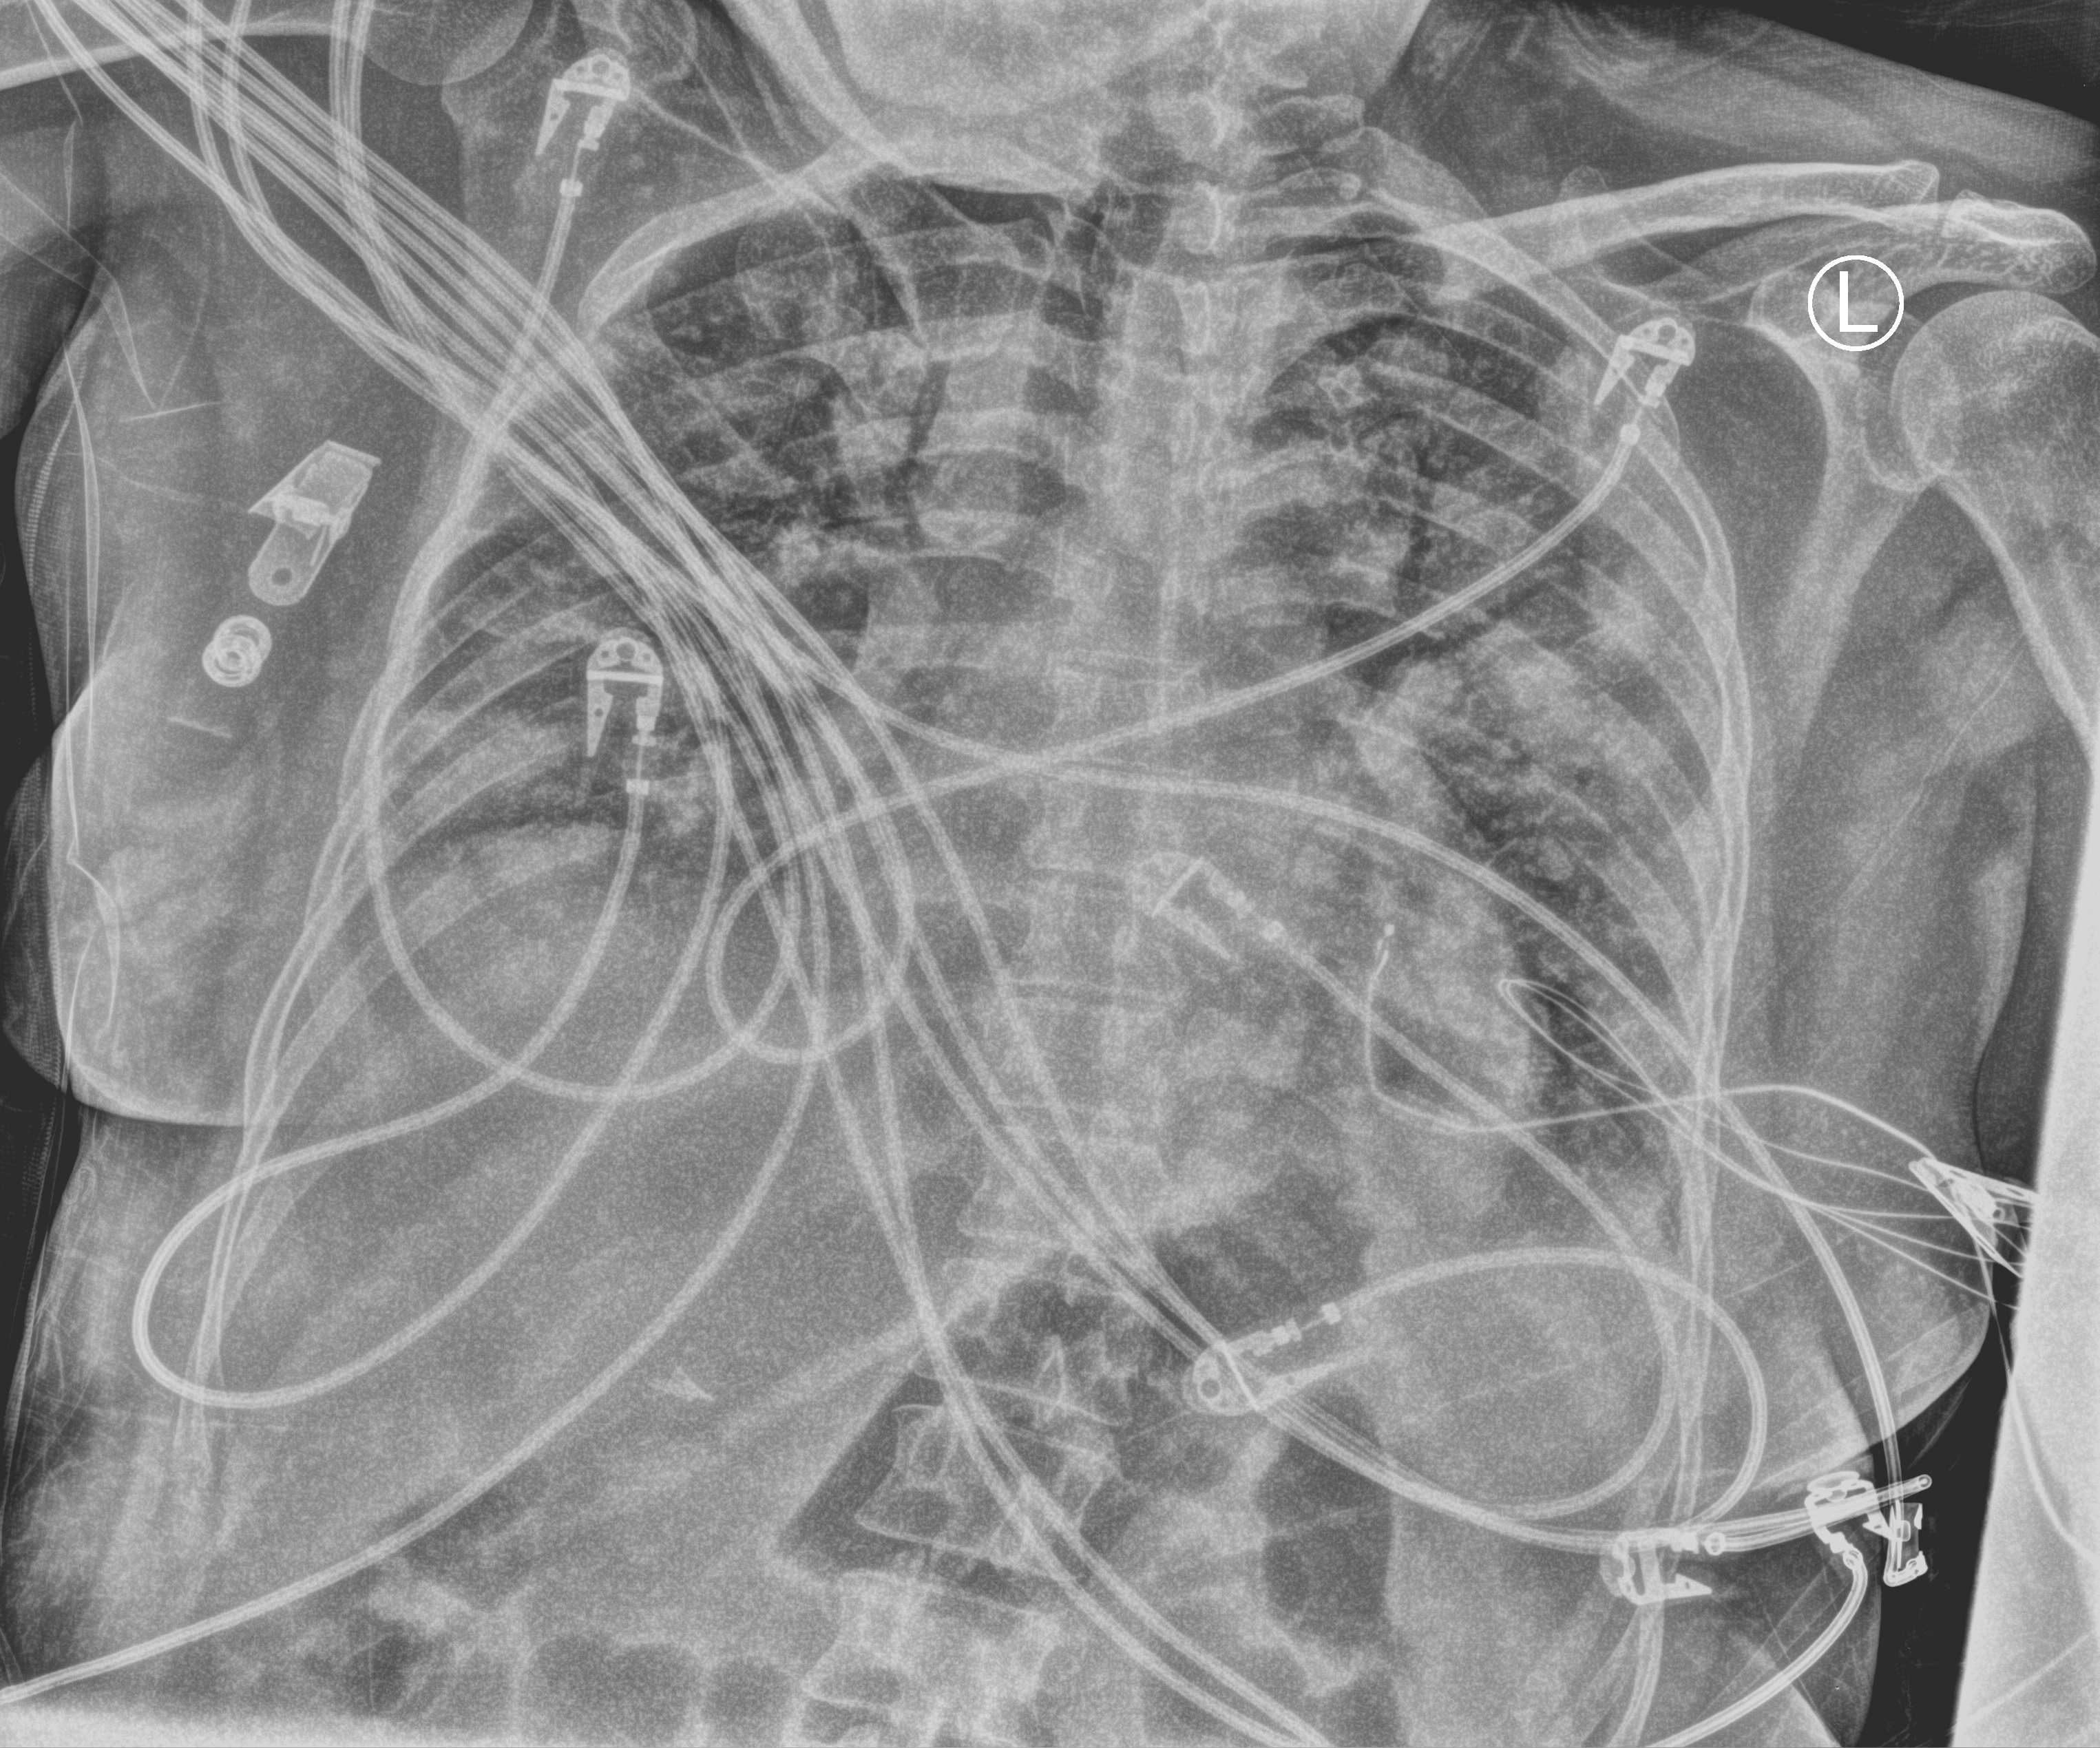
Bedside chest radiograph (computed radiography); anteroposterior (AP) projection. Patient hospitalised with COVID-19; female, aged 18–59 years.
Hospital-stay facts (about this admission, not read from this image; timing relative to this image not recorded): mechanically ventilated during this hospital stay: yes.